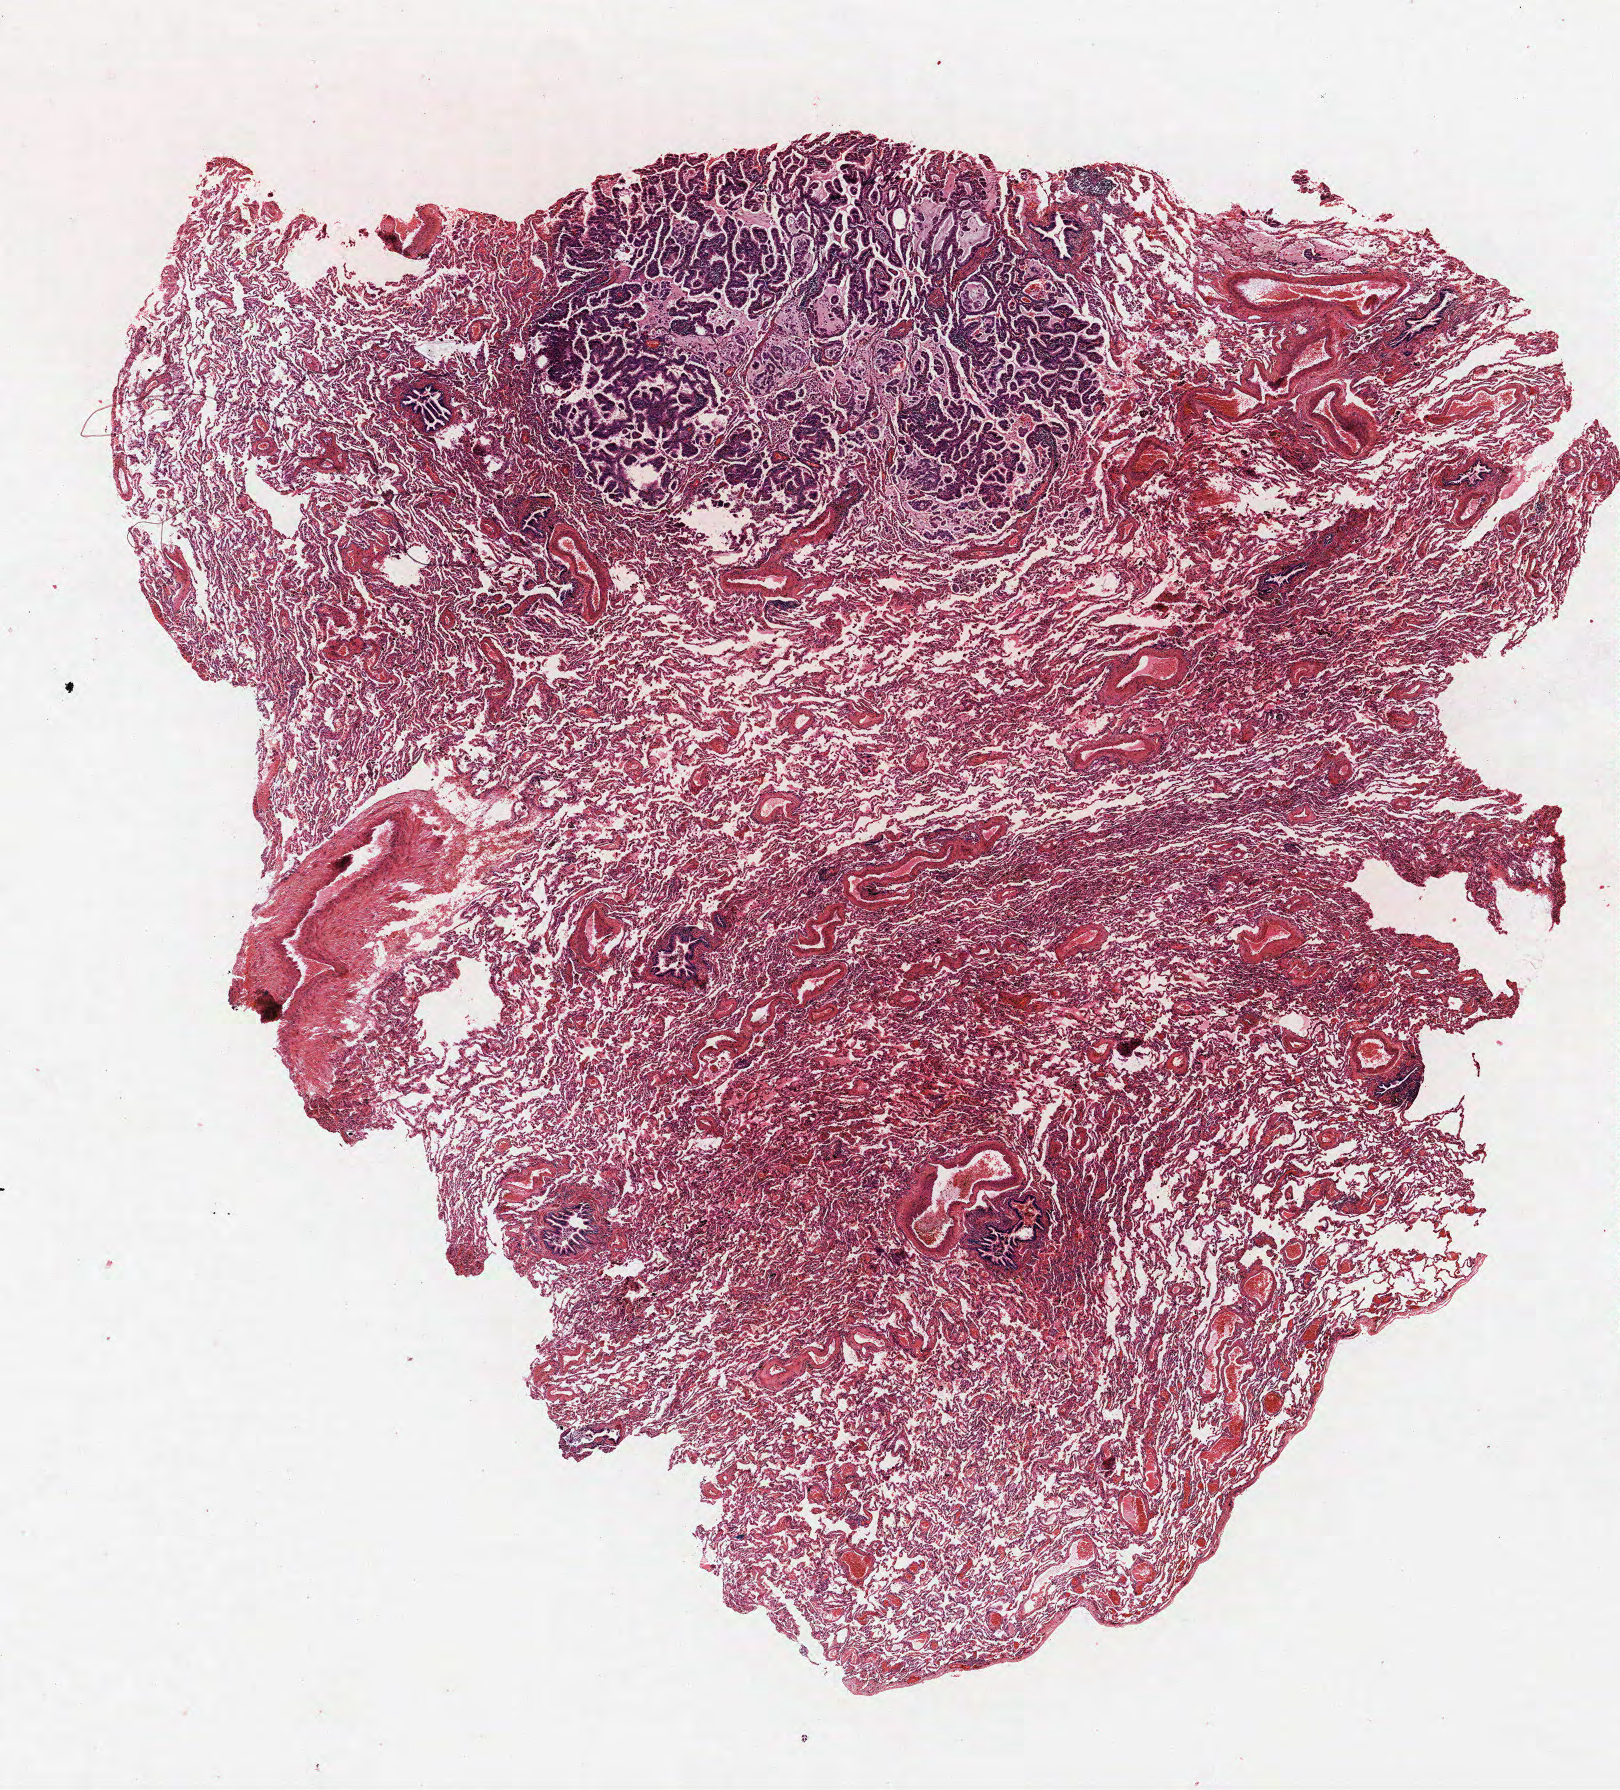
Whole-slide histology image, H&E, low-resolution overview of the scanned area, about 13.0 x 14.3 mm (acquisition: 40x scan); FFPE section; lung. Male patient, aged 55 at enrolment. Former smoker at enrolment. Grade: moderately differentiated (G2).
• ICD-O-3 topography: upper lobe of lung (C34.1)
• primary tumour location (clinical record): right upper lobe
• participant's lung-cancer diagnosis: Acinar cell carcinoma (ICD-O-3 8550/3)
• stage (AJCC 6th edition): IA
• tumour size (pathology): 15 mm
• note: participant had 2 primary lung cancers recorded; fields above describe the first